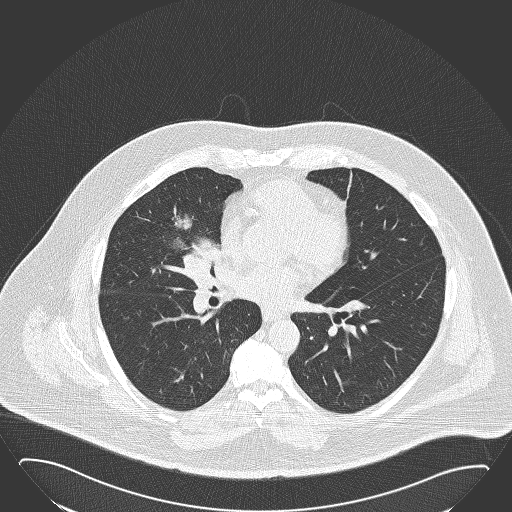
Chest CT (low-dose screening protocol), one axial image; baseline screening round; lung window (W 1500 / L -600 HU); 2 mm slice thickness; 120 kVp. Male participant, aged 61 years at enrolment. Former smoker at enrolment.
- Lesion marked by an expert reader, bounding box <147,205,231,291> (left, top, right, bottom; pixels).
- The screening reader recorded 2 non-calcified nodules or masses ≥4 mm on this exam; which of them this box marks is not recorded.